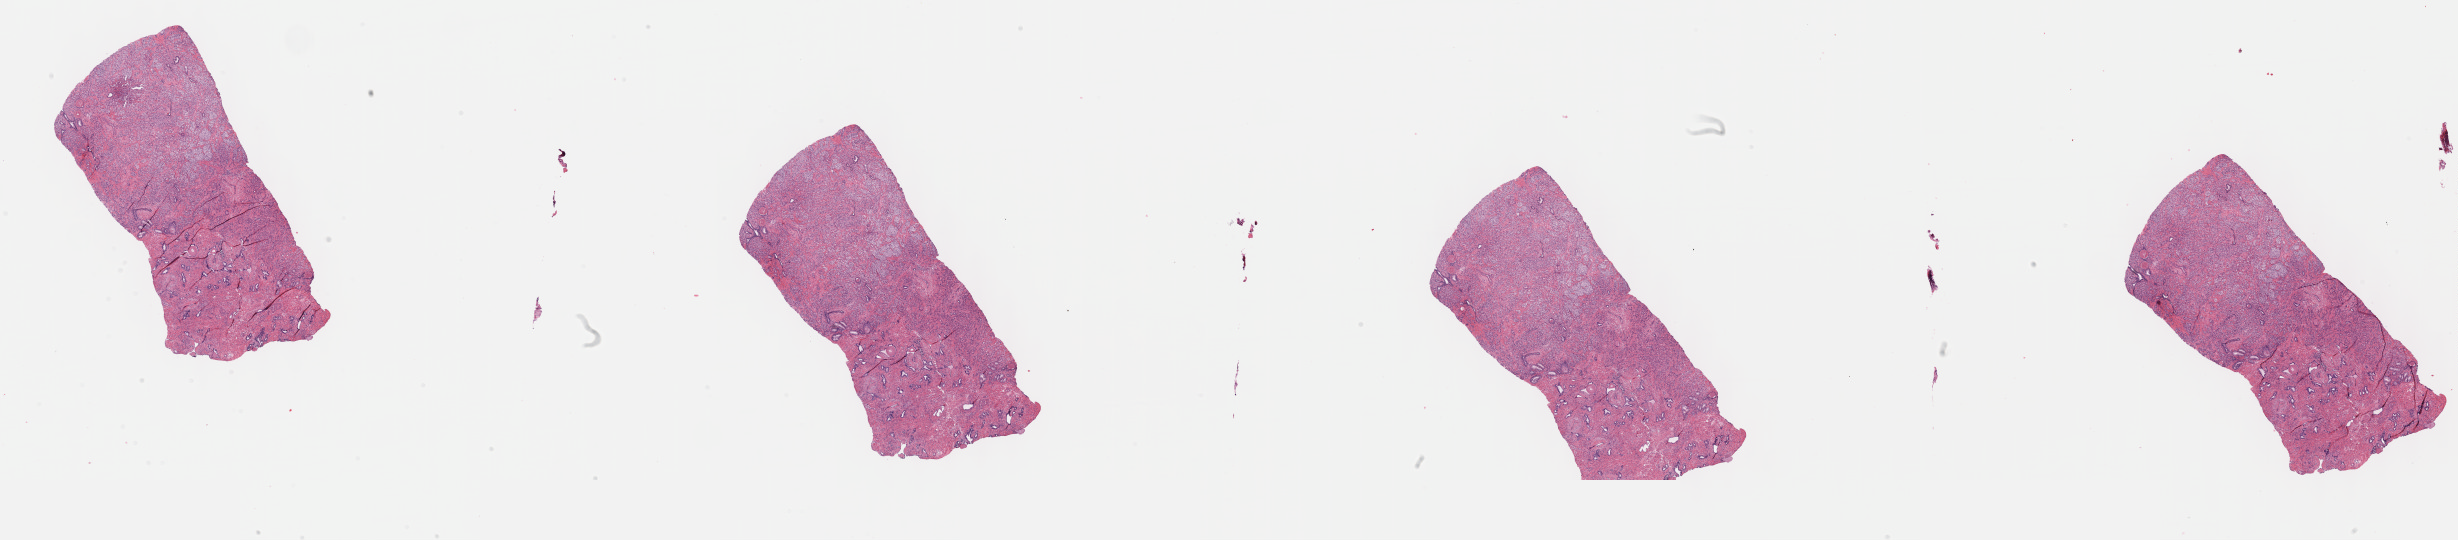
H&E-stained whole-slide image — shown as a low-resolution overview of the whole scanned area (about 39.8 x 8.7 mm, acquisition: 40x scan); FFPE section; prostate, primary tumour sample. Male, age 75 years at initial diagnosis. Gleason score: 8 (4+4). Pathologist review of this section (percent, as recorded): tumour cells 60%, tumour nuclei 70%, normal cells 15%, stromal cells 25%, necrosis 0%. Inflammatory infiltration, as recorded: lymphocyte infiltration 0%, monocyte infiltration 0%, neutrophil infiltration 0%.
* laterality: bilateral
* histologic diagnosis: Adenocarcinoma, NOS (prostate gland)
* lymph nodes positive (case pathology): 0 of 10 examined